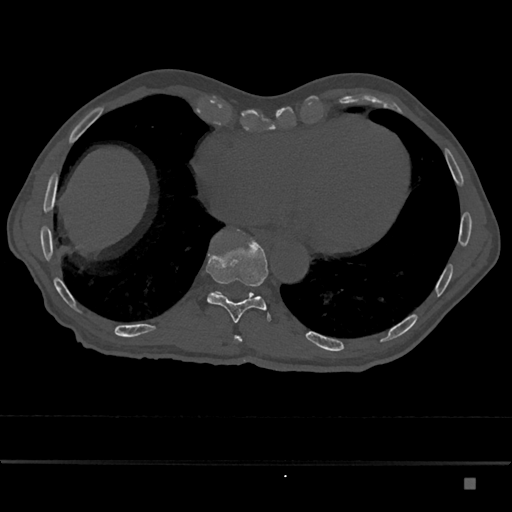
CT including the spine, one axial slice; position 735 of 797 along the scan axis; reconstruction kernel Br40s/3; bone window (W 1800 / L 400 HU); 0.5 mm slice thickness; 512 × 512 image matrix, field of view 390 × 390 mm. Patient: male, 72 years. From the clinical record (not read from this slice): primary cancer: prostate.
Structures marked on this image (semi-automatic segmentation, software-assisted and operator-edited):
- T10 vertebra: bounding box (x1, y1, x2, y2) in pixels: (206, 235, 271, 323)
- T11 vertebra: (215, 291, 253, 296)
- T9 vertebra: (234, 335, 242, 342)